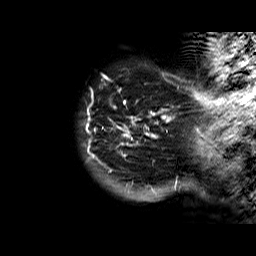
Breast MRI (dynamic contrast-enhanced), one sagittal slice; position 2 of 60 along the scan axis; dynamic contrast-enhanced series, time point 2 of 6 at this slice position (early post-contrast); 1.5 T; TE 6.3 ms, TR 32.4 ms; 4 mm slice thickness; 256 × 256 image matrix, field of view 200 × 200 mm. Female patient. From the clinical record (not read from this slice): setting: breast cancer imaged before/during neoadjuvant chemotherapy; receptor status: HR-positive, HER2-negative.
Annotated regions visible in this slice (semi-automatic segmentation, software-assisted and operator-edited):
- analysis volume of interest (the breast-tissue region the enhancement analysis was run in; not a lesion): bounding box [x1, y1, x2, y2] px = [82, 73, 177, 183]
- tumour enhancement mask (voxels above the 100 % enhancement threshold inside the analysis volume of interest): [86, 76, 172, 158]